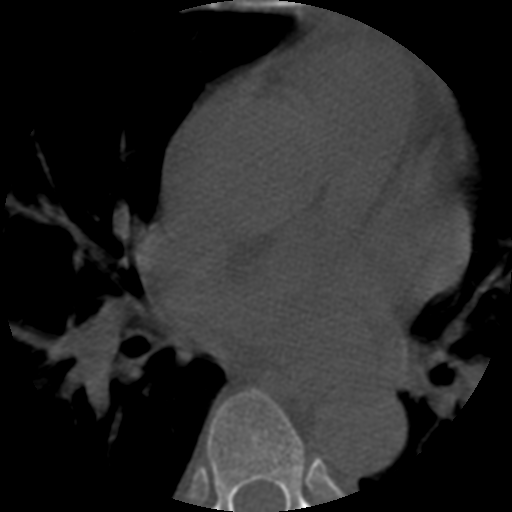
CT including the spine, one axial slice; slice 358 of 508 in the series (ordered by position); reconstruction kernel STANDARD; 120 kVp; bone window (W 1800 / L 400 HU); 1.25 mm slice thickness; 512 × 512 image matrix, field of view 160 × 160 mm. Patient age 57 years. From the clinical record (not read from this slice): primary cancer: prostate.
Structures marked on this image (semi-automatically segmented with operator editing):
- T6 vertebra: box from (x=207, y=389) to (x=309, y=512) px